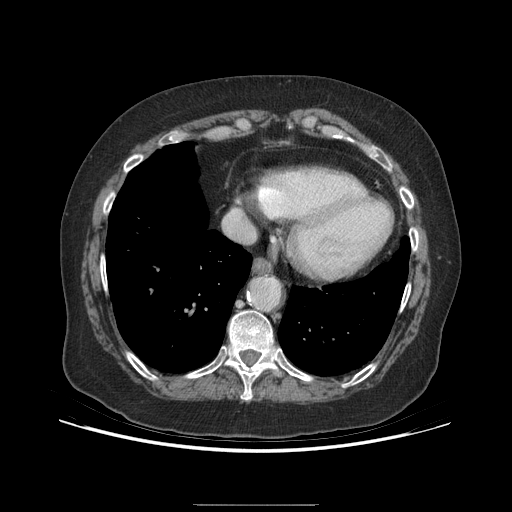
Contrast-enhanced abdominal CT (liver protocol), one axial slice; slice 185 of 192 in the series (ordered by position); soft-tissue window (W 400 / L 40 HU); 2.5 mm slice thickness; 512 × 512 image matrix. From the clinical record (not read from this slice): diagnosis: hepatocellular carcinoma (patient treated with transarterial chemoembolisation; whether this scan precedes or follows treatment is not stated here); TNM stage (as recorded): Stage-I; Child-Pugh class: A; tumour differentiation: moderately differentiated; tumour nodularity: uninodular.
Annotated regions visible in this slice (semi-automatic segmentation, software-assisted and operator-edited):
- abdominal aorta: bounding box <251,278,279,308> (left, top, right, bottom; pixels)